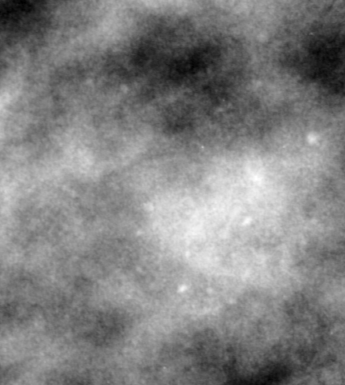
Region of interest cut from a scanned film mammogram (one marked finding), right breast, CC view.
Finding: calcifications, morphology pleomorphic, distribution clustered; BI-RADS assessment category 4; subtlety rating 2 on a 1 (subtle) to 5 (obvious) scale; pathology (as recorded): benign.